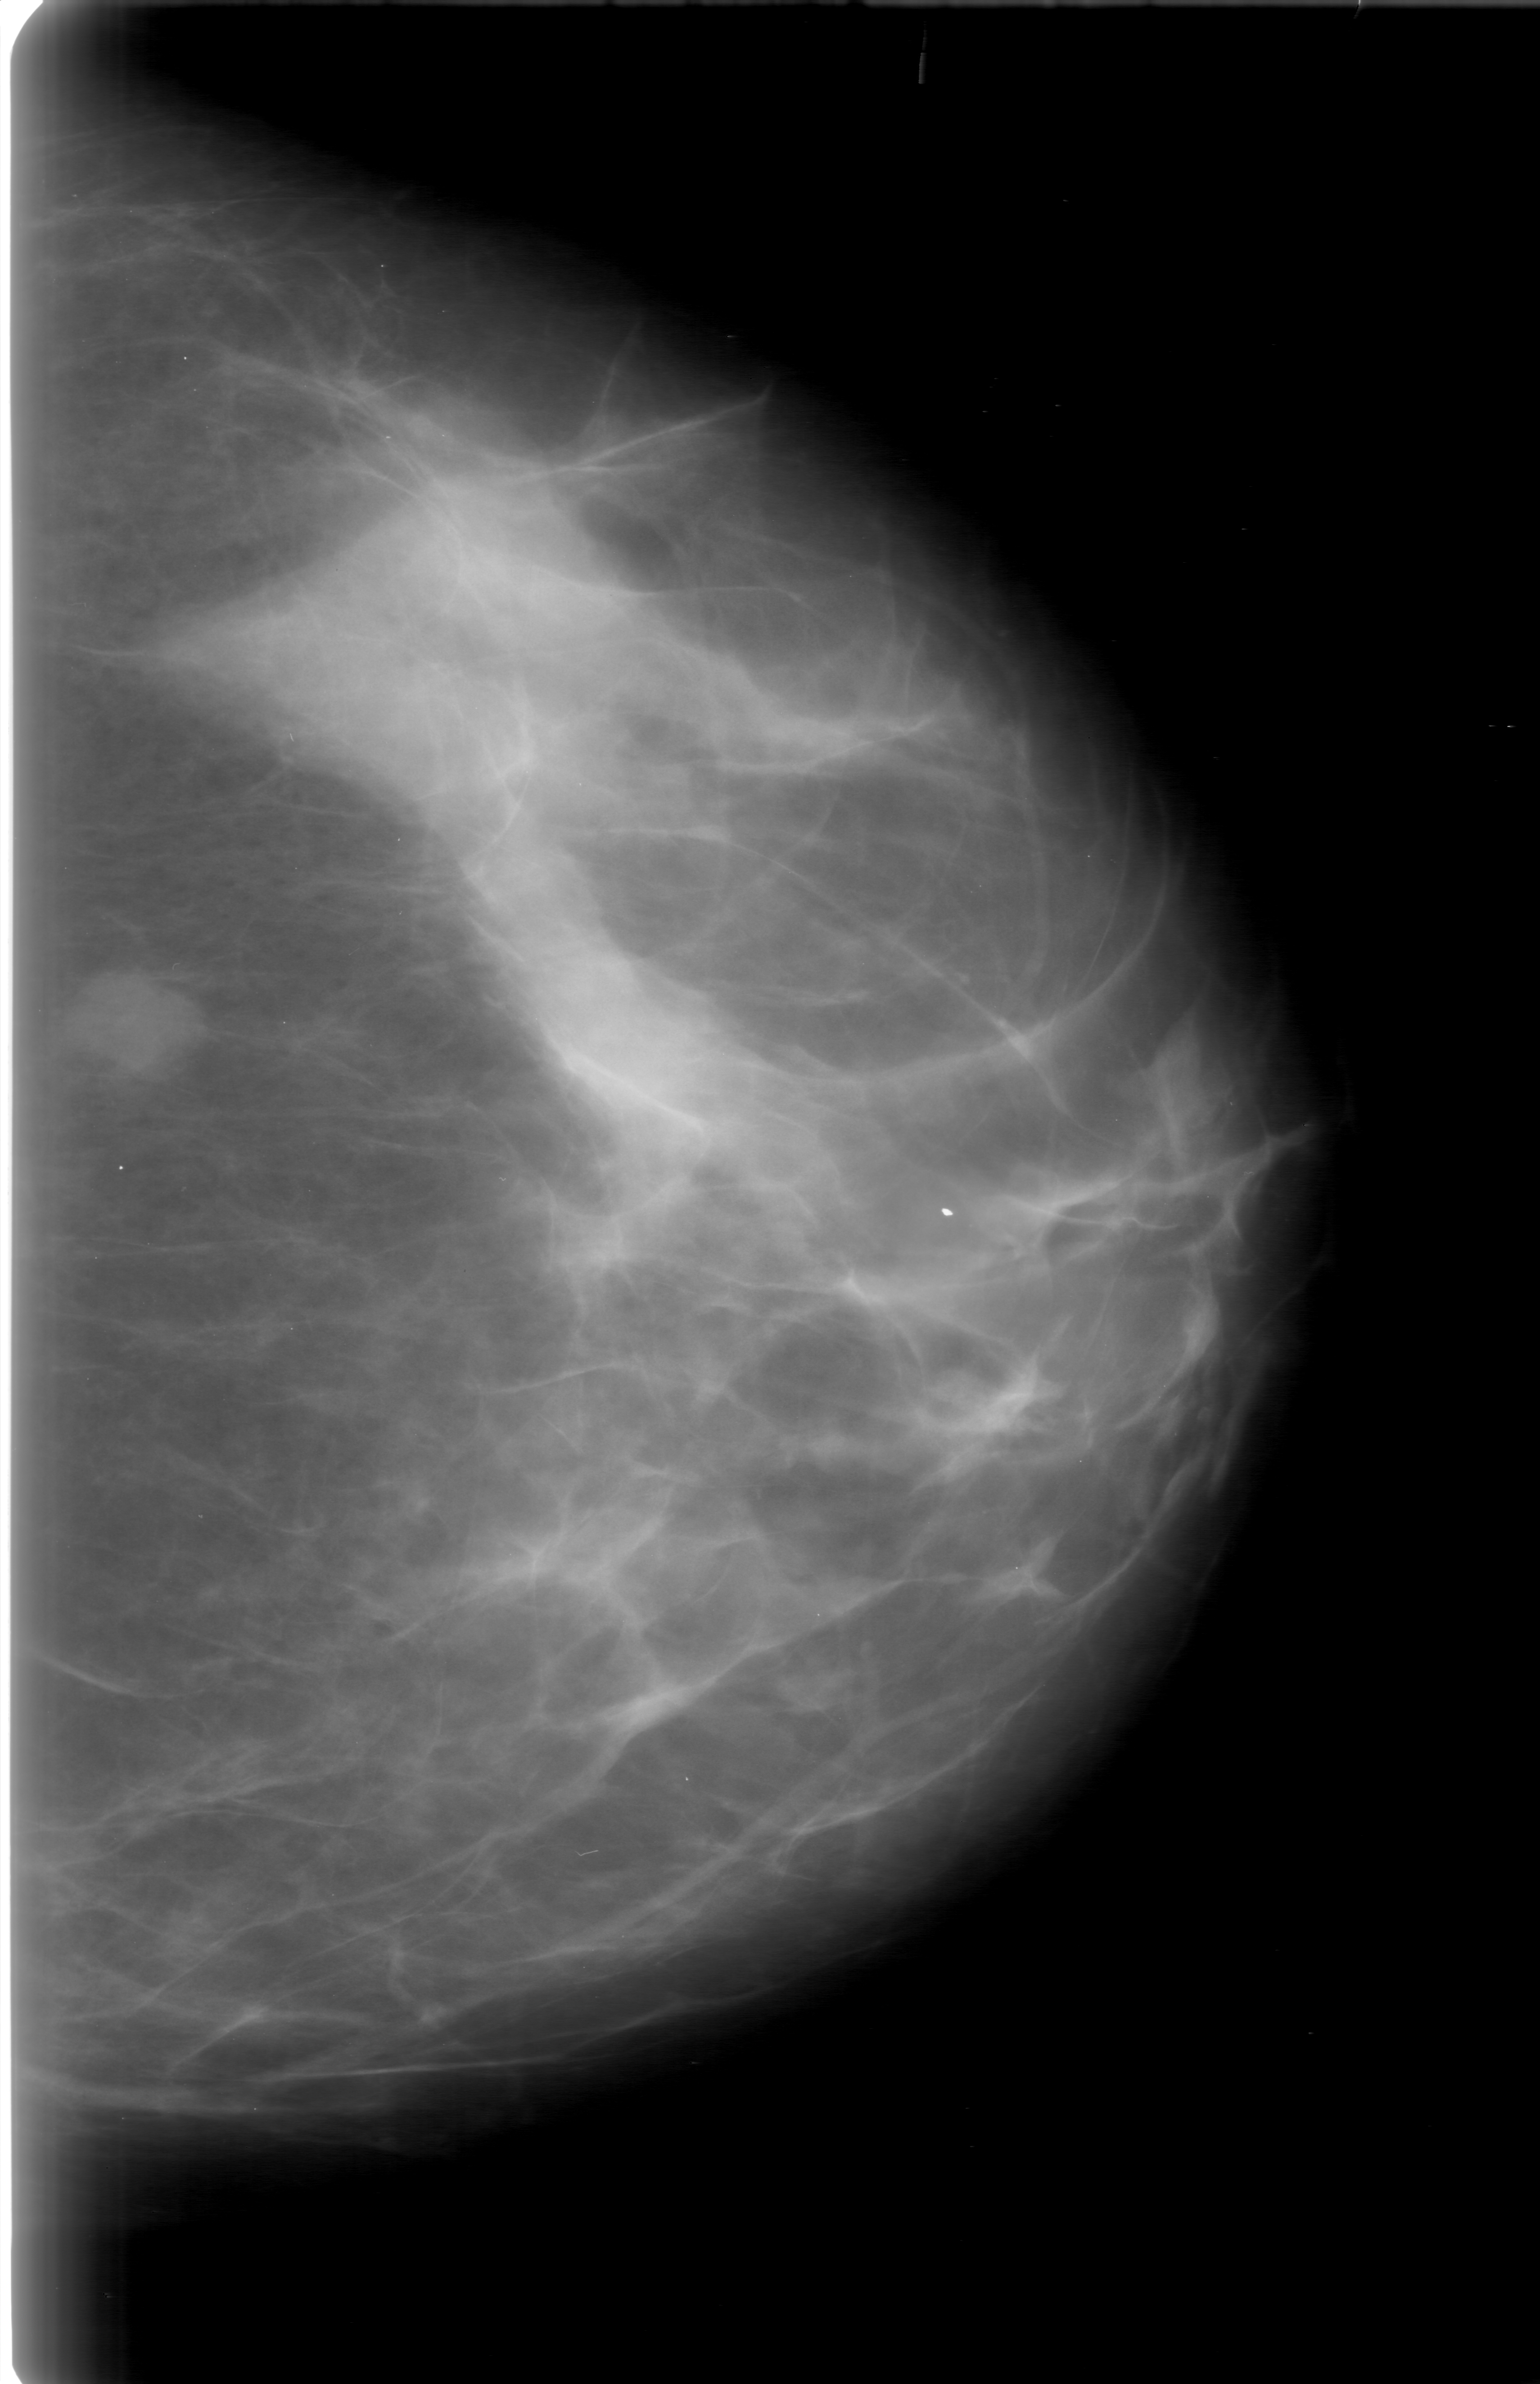
Digitized screen-film mammogram, left breast, CC view, breast composition: heterogeneously dense (BI-RADS density category 3 of 4).
Marked abnormality: mass, shape oval, margins obscured; BI-RADS assessment category 0 (incomplete: needs additional imaging); pathology result (as recorded, not read from the image): benign.